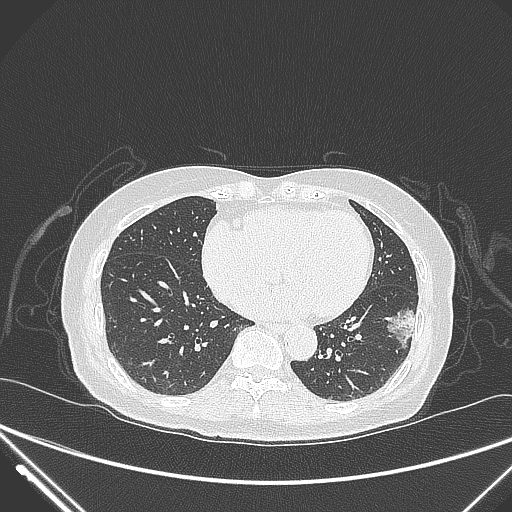
Chest CT, one axial slice; position 112 of 310 along the scan axis; 120 kVp; lung window (W 1500 / L -600 HU); 1 mm slice thickness; 512 × 512 image matrix, field of view 377 × 377 mm. Patient: female, 82 years. From the clinical record (not read from this slice): clinical TNM (as recorded): T1c N0 M0.
Structures marked on this image (rectangle marked by the reading radiologist):
- lung tumour (recorded histology: adenocarcinoma): bounding box <384,298,424,353> (left, top, right, bottom; pixels)